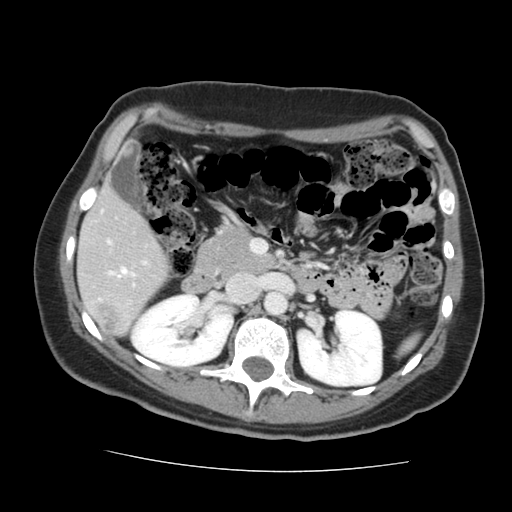
Contrast-enhanced abdominal CT, one axial slice; position 73 of 144 along the scan axis; intravenous contrast given; soft-tissue window (W 400 / L 40 HU); 2.5 mm slice thickness; 512 × 512 image matrix, field of view 333 × 333 mm. Female patient, age 46 years. From the clinical record (not read from this slice): diagnosis: colorectal cancer liver metastases, imaged before liver resection; multiple liver metastases: no.
Annotated regions visible in this slice (manually delineated by an expert):
- liver: box from (x=78, y=189) to (x=170, y=335) px
- planned liver remnant (the part of the liver to remain after resection): (x=78, y=189)–(x=170, y=335)
- portal vein (with intrahepatic branches): (x=107, y=241)–(x=145, y=278)
- liver metastasis: (x=100, y=303)–(x=117, y=330)